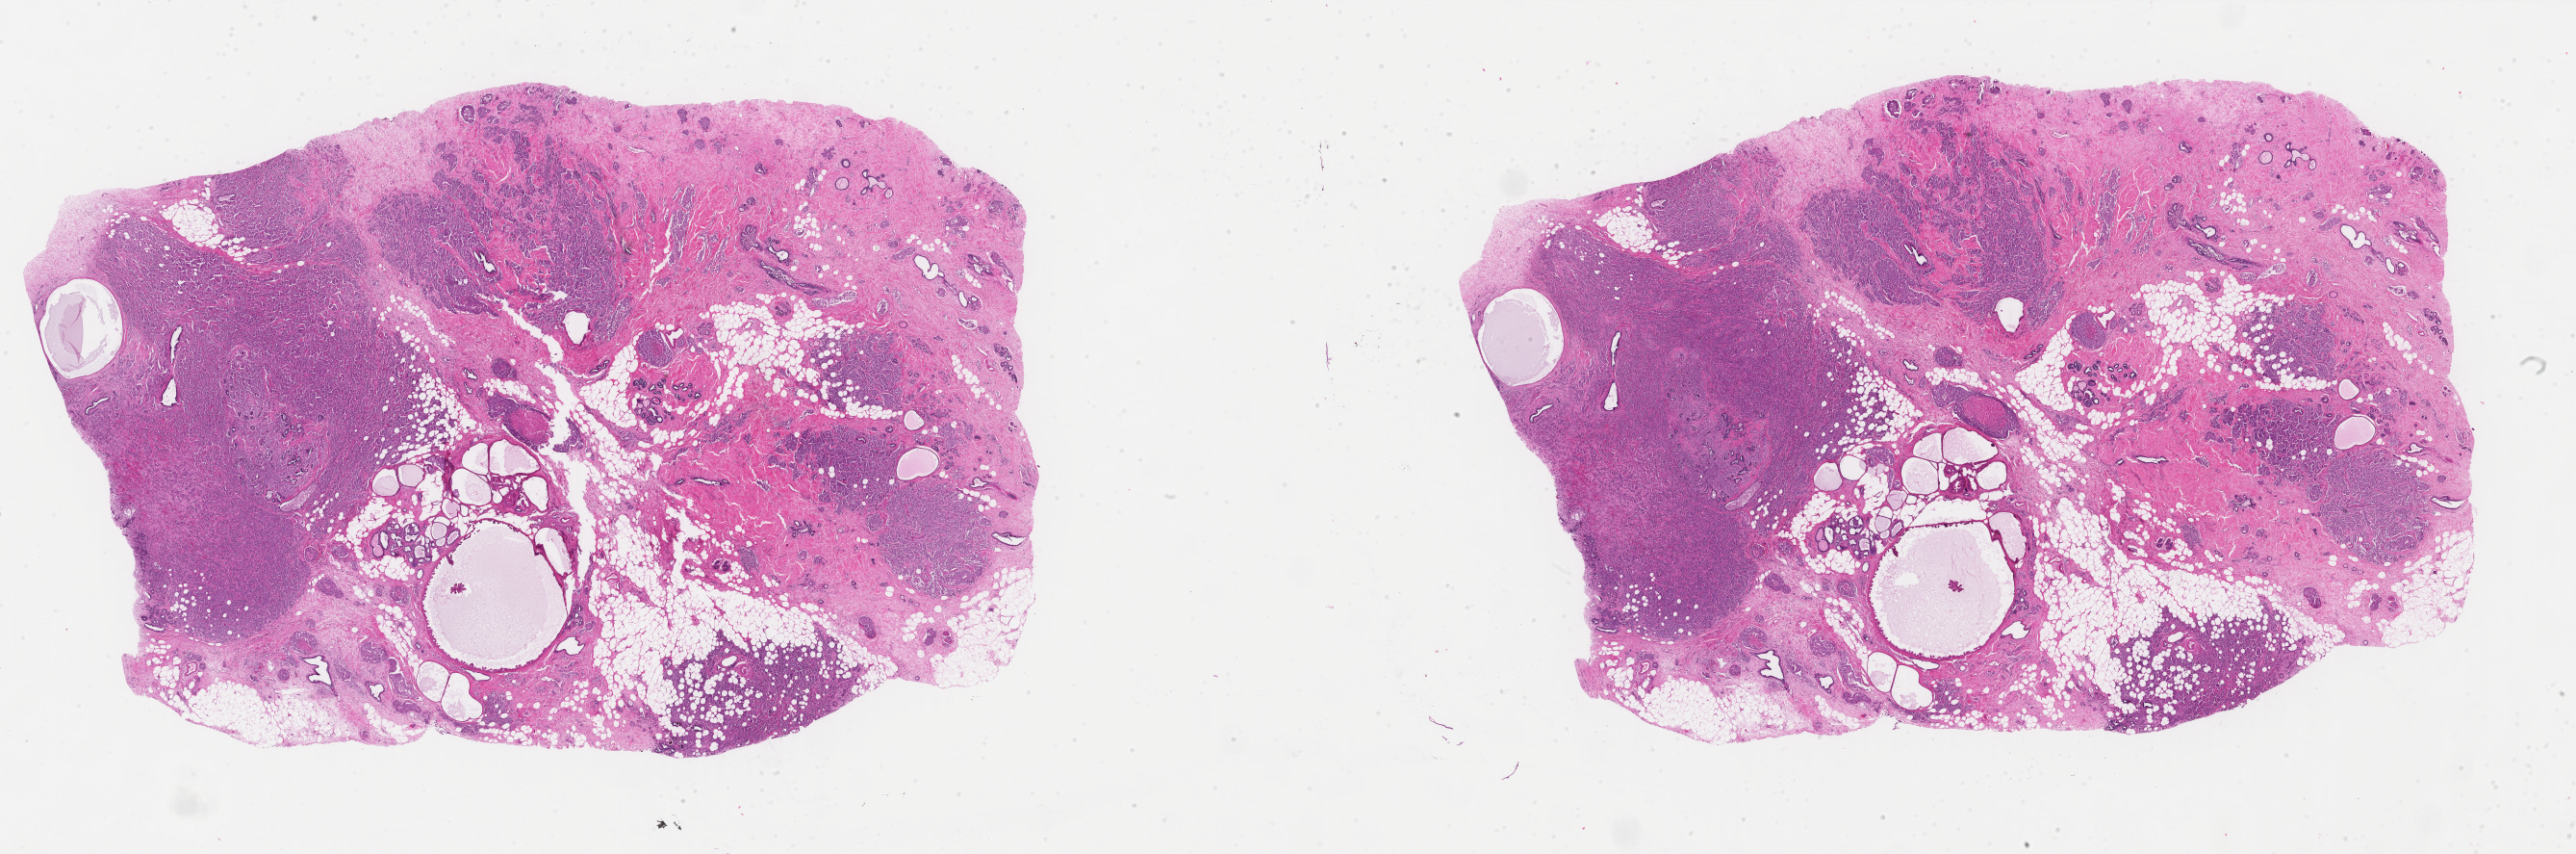
H&E-stained whole-slide image — a low-resolution overview of the entire scanned area, about 42.5 x 14.1 mm, FFPE section, sample: primary tumour, breast. Female, age 63 years at initial diagnosis.
Pathologic diagnosis: Infiltrating duct carcinoma, NOS. Lymph nodes positive (case pathology): 8 of 9 examined. AJCC pathologic stage: IV.